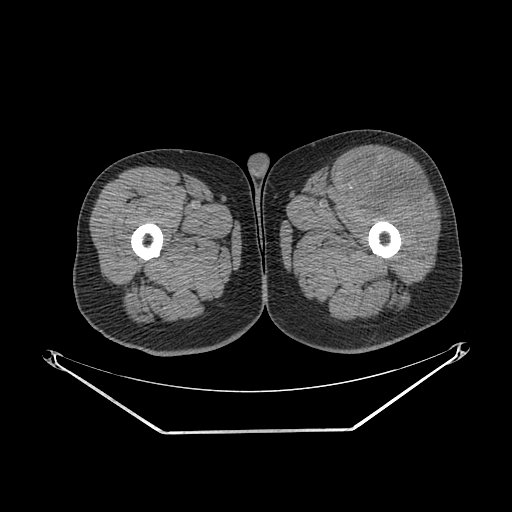
CT of an extremity soft-tissue mass (from a PET/CT study), one axial slice. Position 244 of 267 along the scan axis. Reconstruction kernel SOFT. 140 kVp. Soft-tissue window (W 400 / L 40 HU). 3.75 mm slice thickness. 512 × 512 image matrix, field of view 500 × 500 mm. Male patient. From the clinical record (not read from this slice): histological type: extraskeletal osteosarcoma; grade: high; site of the primary tumour: thigh.
Annotated regions visible in this slice (expert contour drawn on MRI and transferred to this co-registered scan by the dataset authors):
- gross tumour volume (mass): bounding box [x1, y1, x2, y2] px = [352, 162, 428, 211]